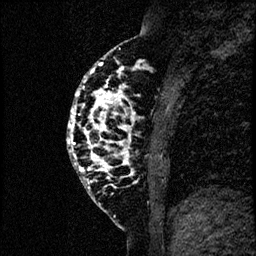
Breast MRI (dynamic contrast-enhanced), one sagittal slice. Position 26 of 60 along the scan axis. Dynamic contrast-enhanced study with each time point stored as its own series, time point 2 of 4 at this slice position (early post-contrast, ordered by acquisition time). 1.5 T. TE 4.2 ms, TR 17.6 ms. 2 mm slice thickness. 256 × 256 image matrix, field of view 200 × 200 mm. Female patient, age 40 years. From the clinical record (not read from this slice): setting: breast cancer imaged before/during neoadjuvant chemotherapy; receptor status: HER2-positive.
Outlined on this slice (semi-automatic segmentation, software-assisted and operator-edited):
- analysis volume of interest (the breast-tissue region the enhancement analysis was run in; not a lesion): box from (x=66, y=55) to (x=184, y=206) px
- tumour enhancement mask (voxels above the 100 % enhancement threshold inside the analysis volume of interest): (x=66, y=62)–(x=138, y=187)